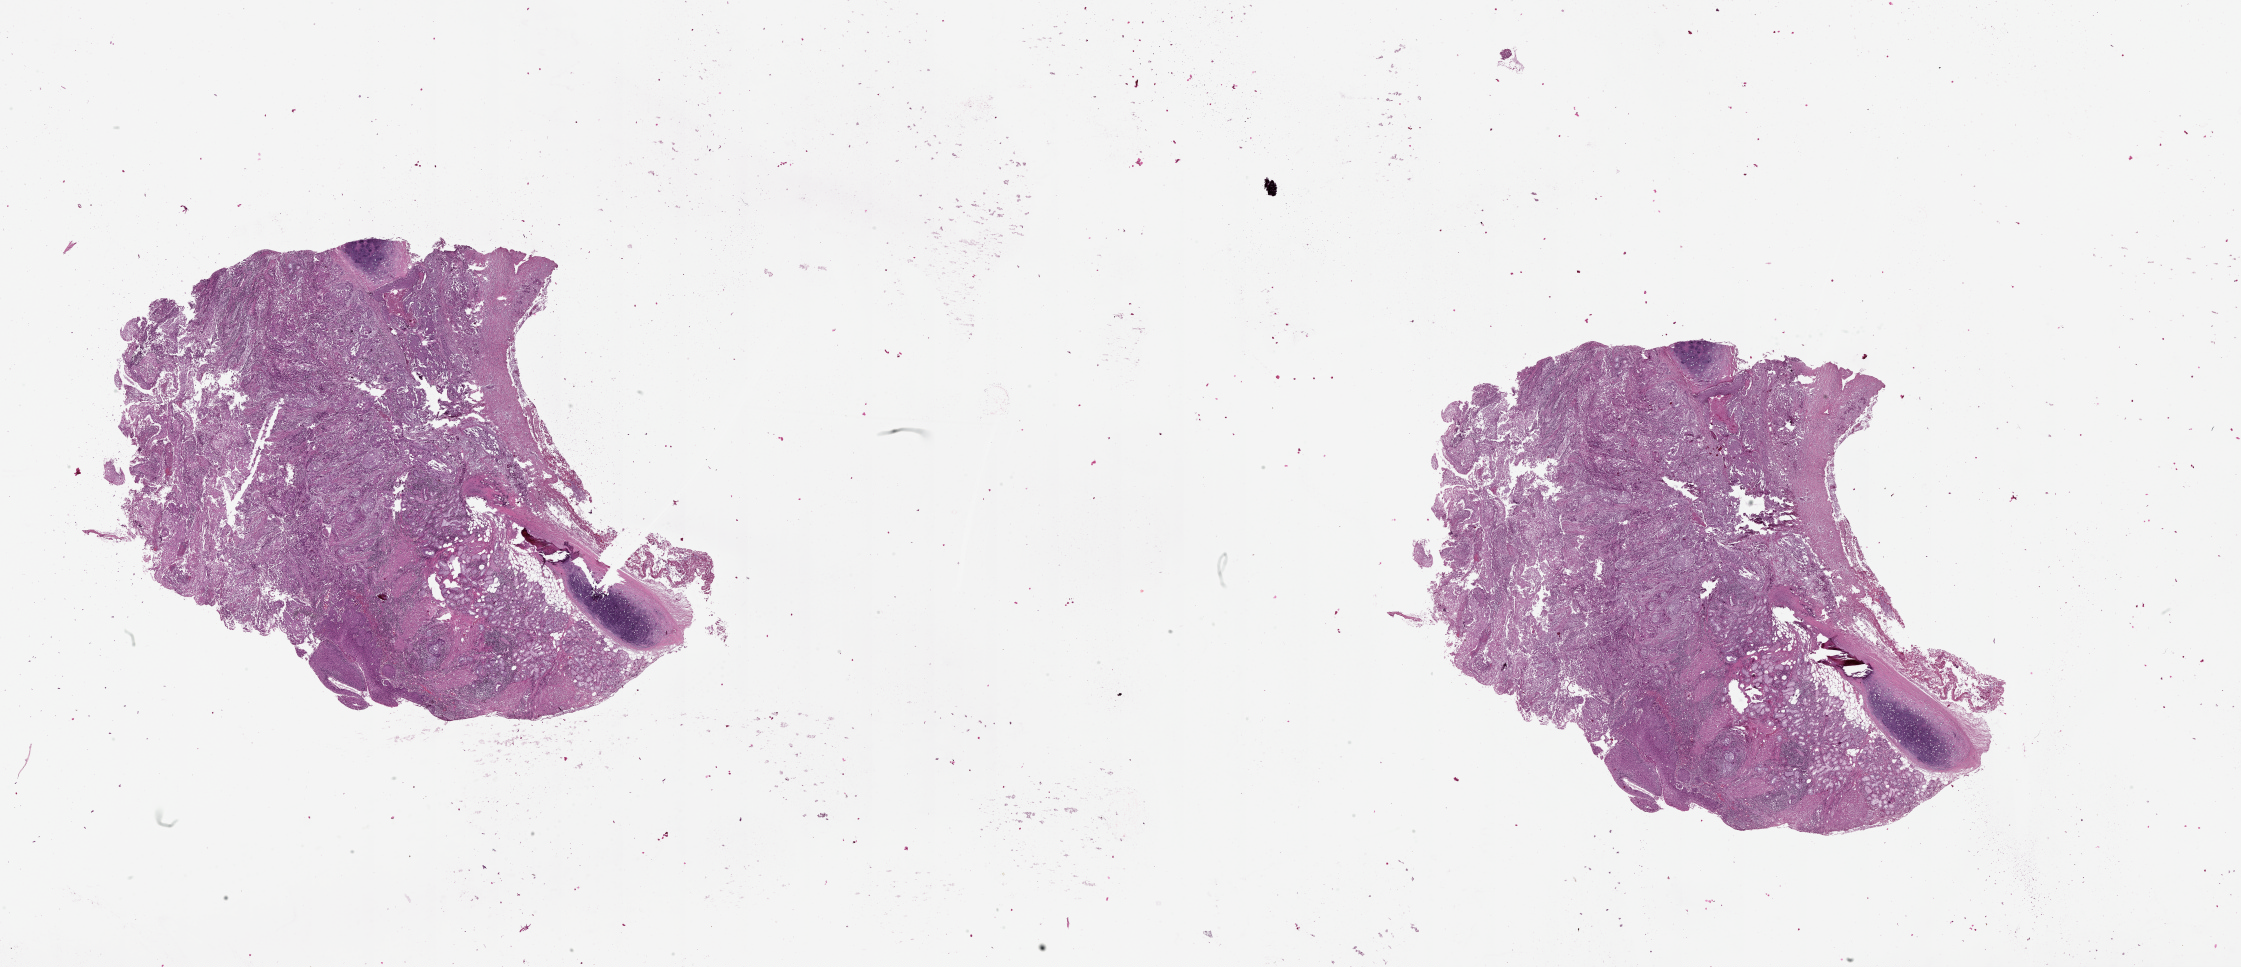
Whole-slide histology image, H&E — low-resolution overview of the scanned area, about 36.1 x 15.6 mm (slide scanned at 20x). Lung, tumour tissue. Patient: male, age 65 years.
Patient diagnosis (cohort enrolment): squamous cell carcinoma (lung).